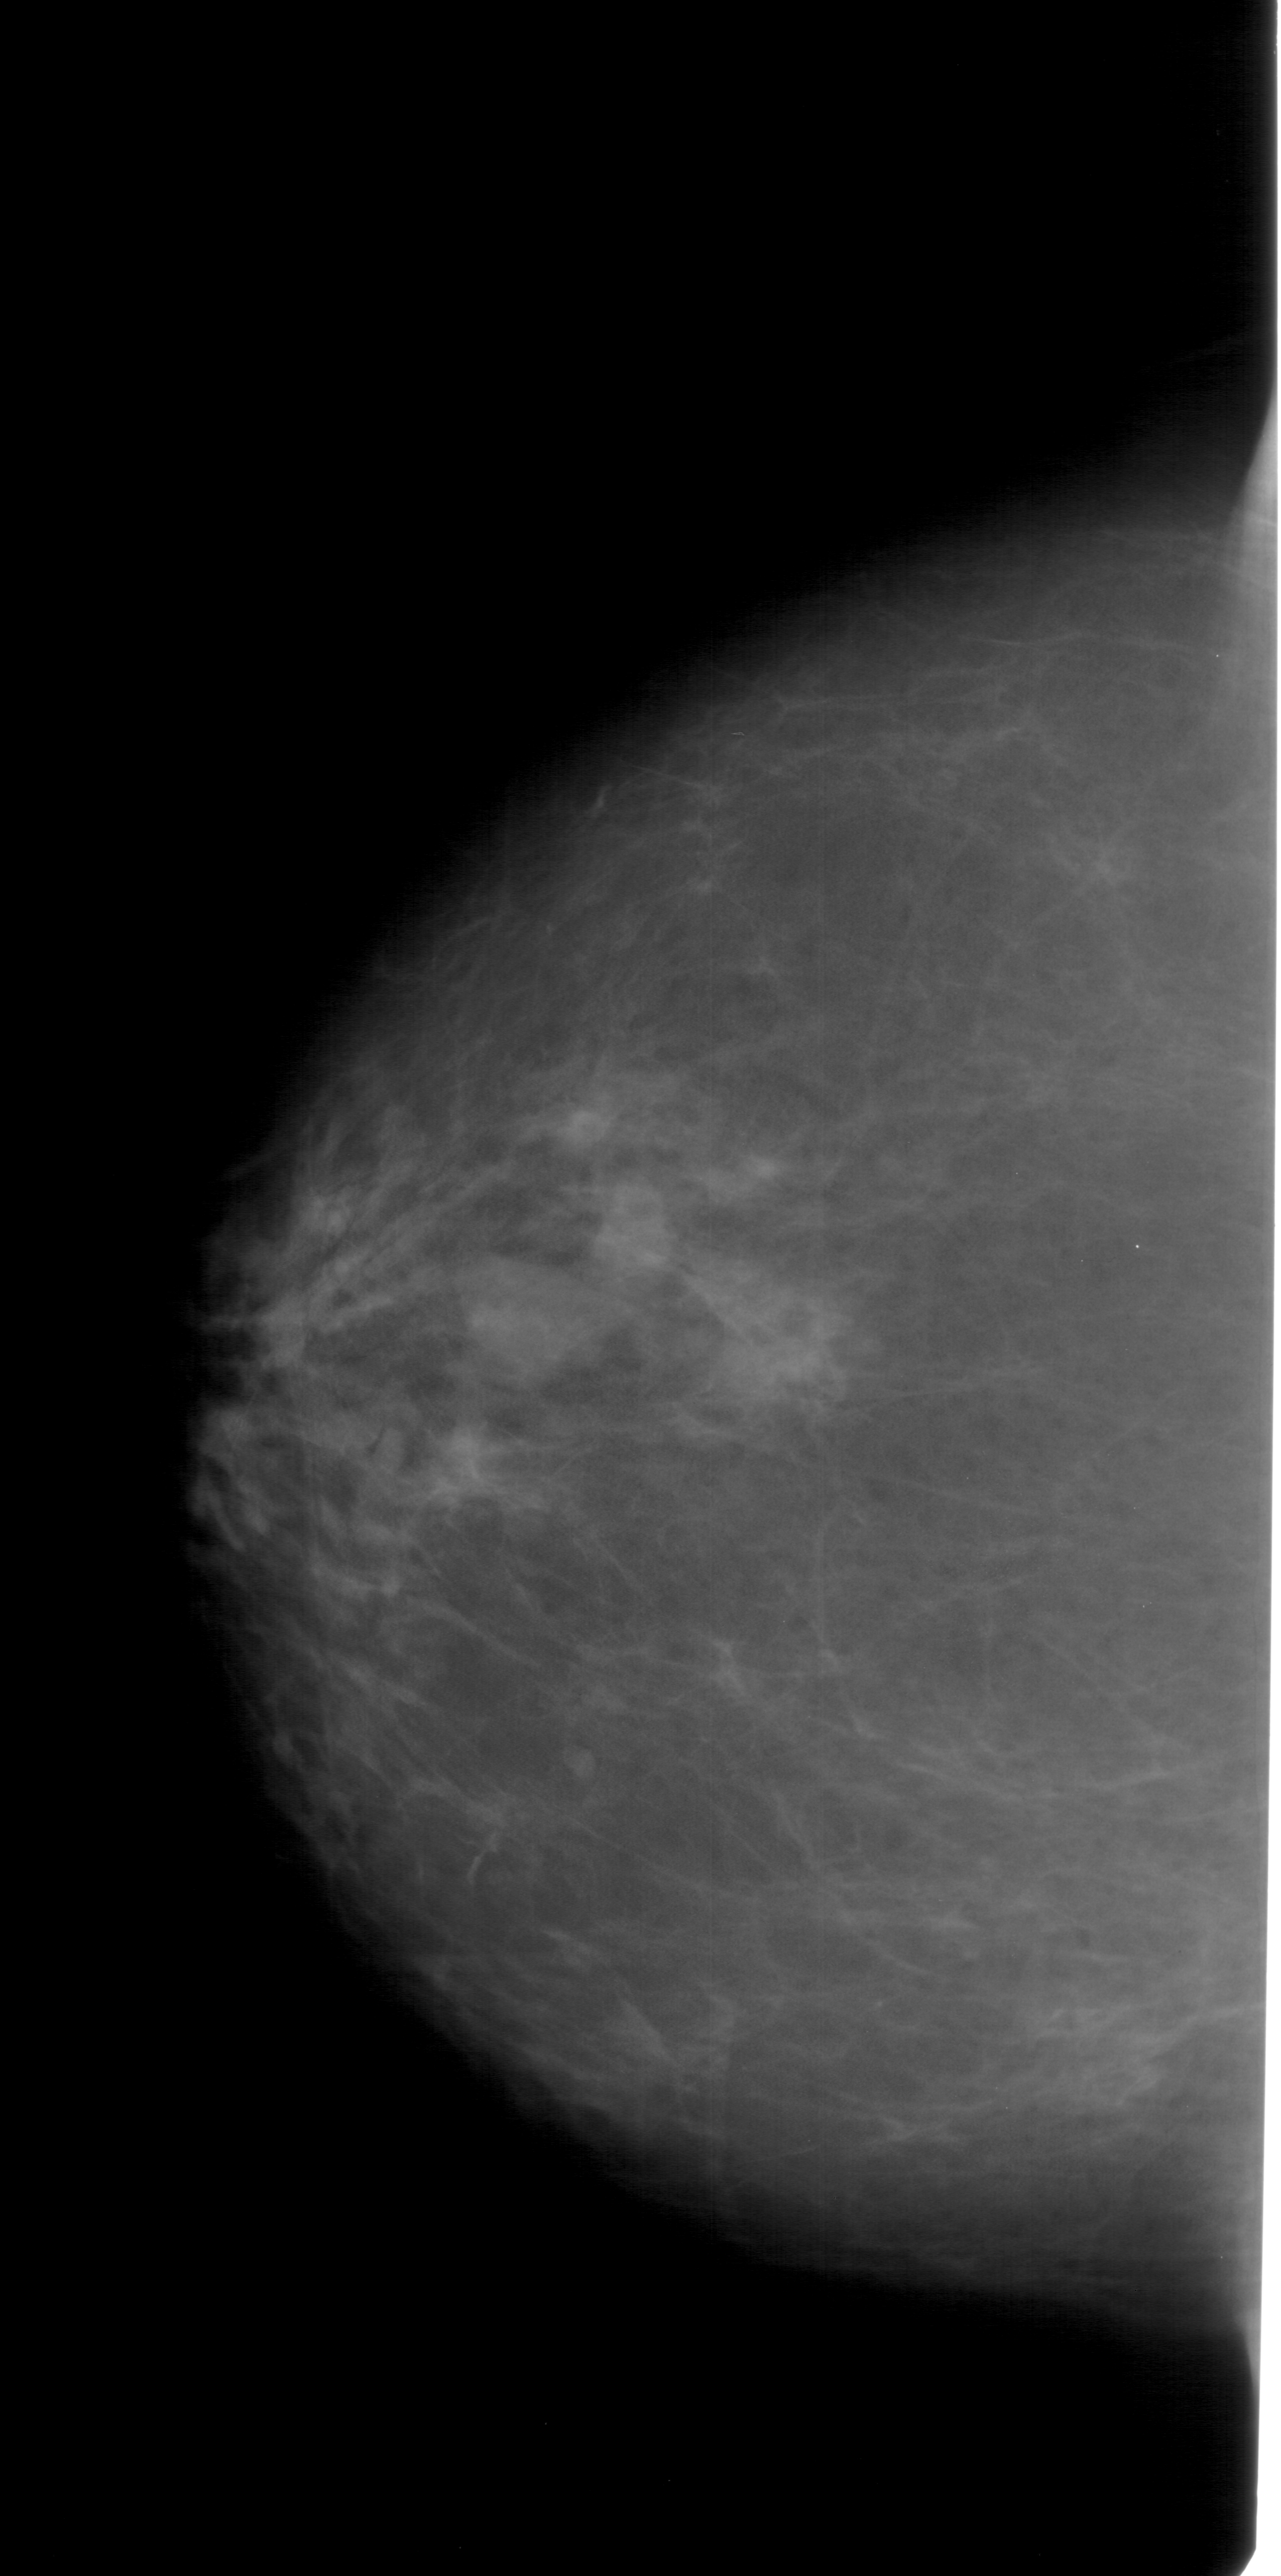
Digitized screen-film mammogram; left breast; CC view; BI-RADS breast density category 2 (scale 1–4).
Abnormality record for this image: mass, shape lobulated, margins ill defined; BI-RADS assessment category 4; subtlety rating 5 on a 1 (subtle) to 5 (obvious) scale; pathology (as recorded): benign.